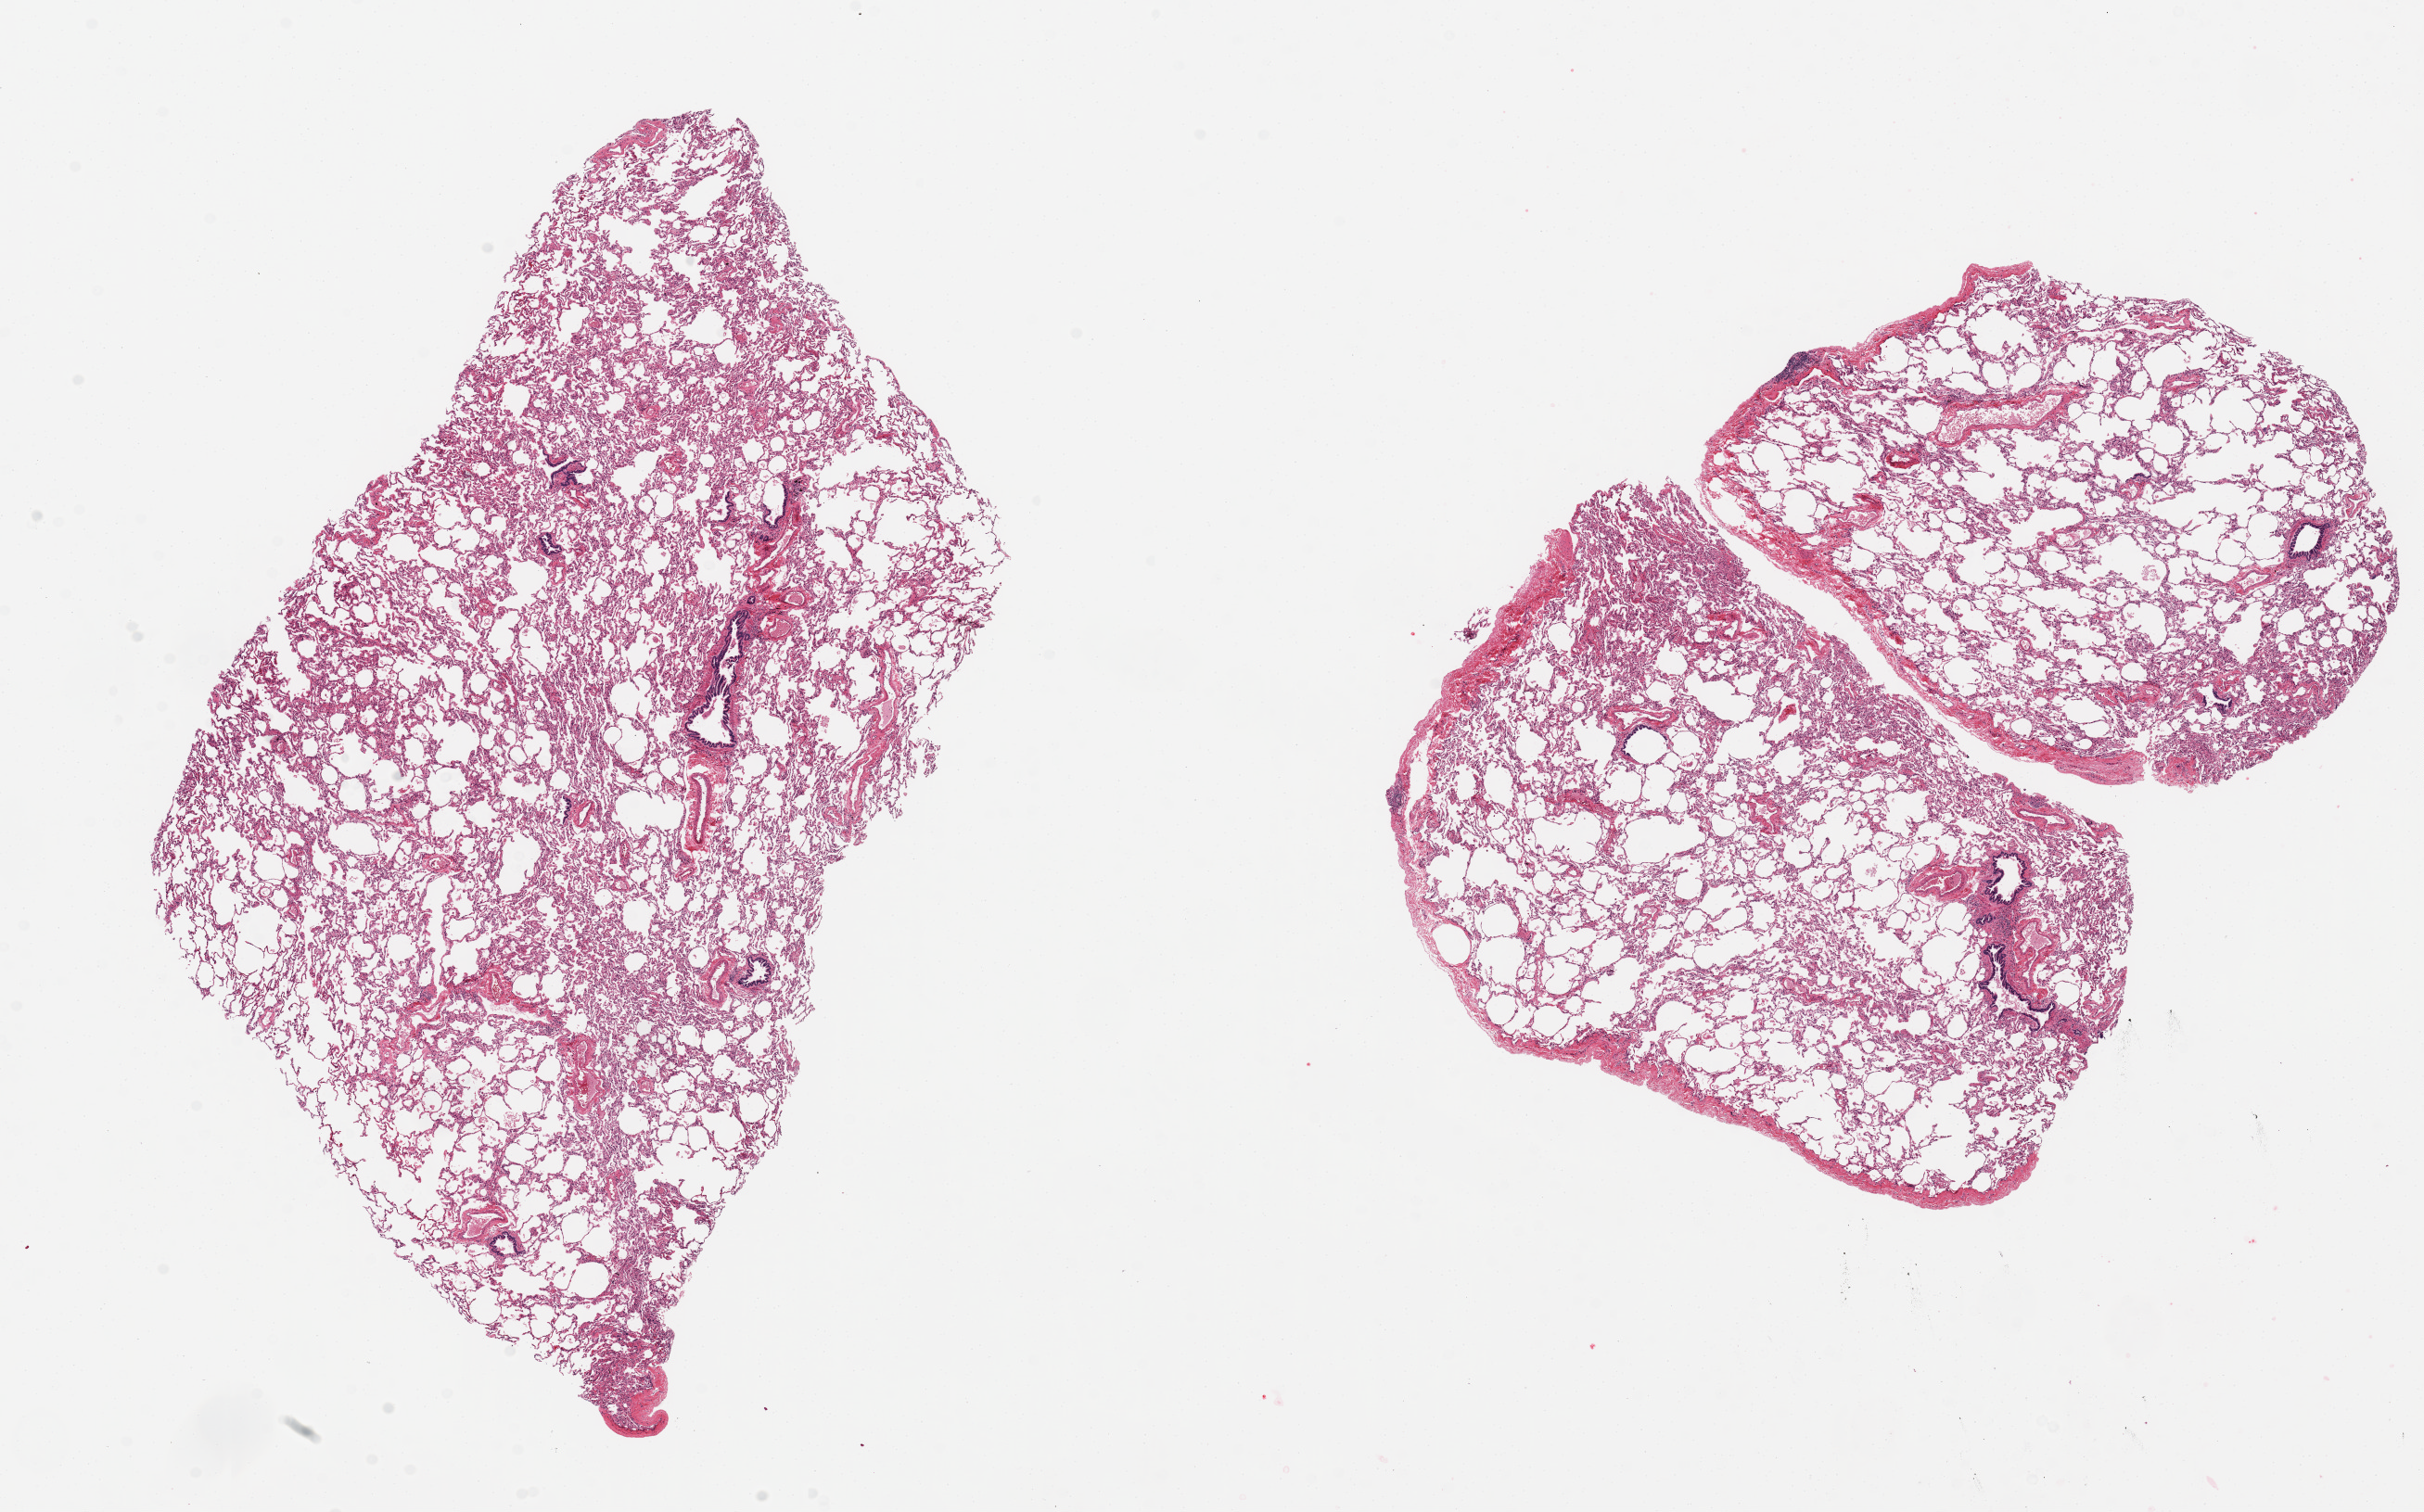
Haematoxylin and eosin whole-slide image, brightfield — a low-resolution overview of the entire scanned area, about 20.7 x 12.9 mm. PAXgene-fixed, paraffin-embedded tissue. Sampled site (target tissue): lung. Donor tissue sample.
Pathologist's review note for this sample: 2 pieces ~8x6 mm; good morphology, no inflammation.